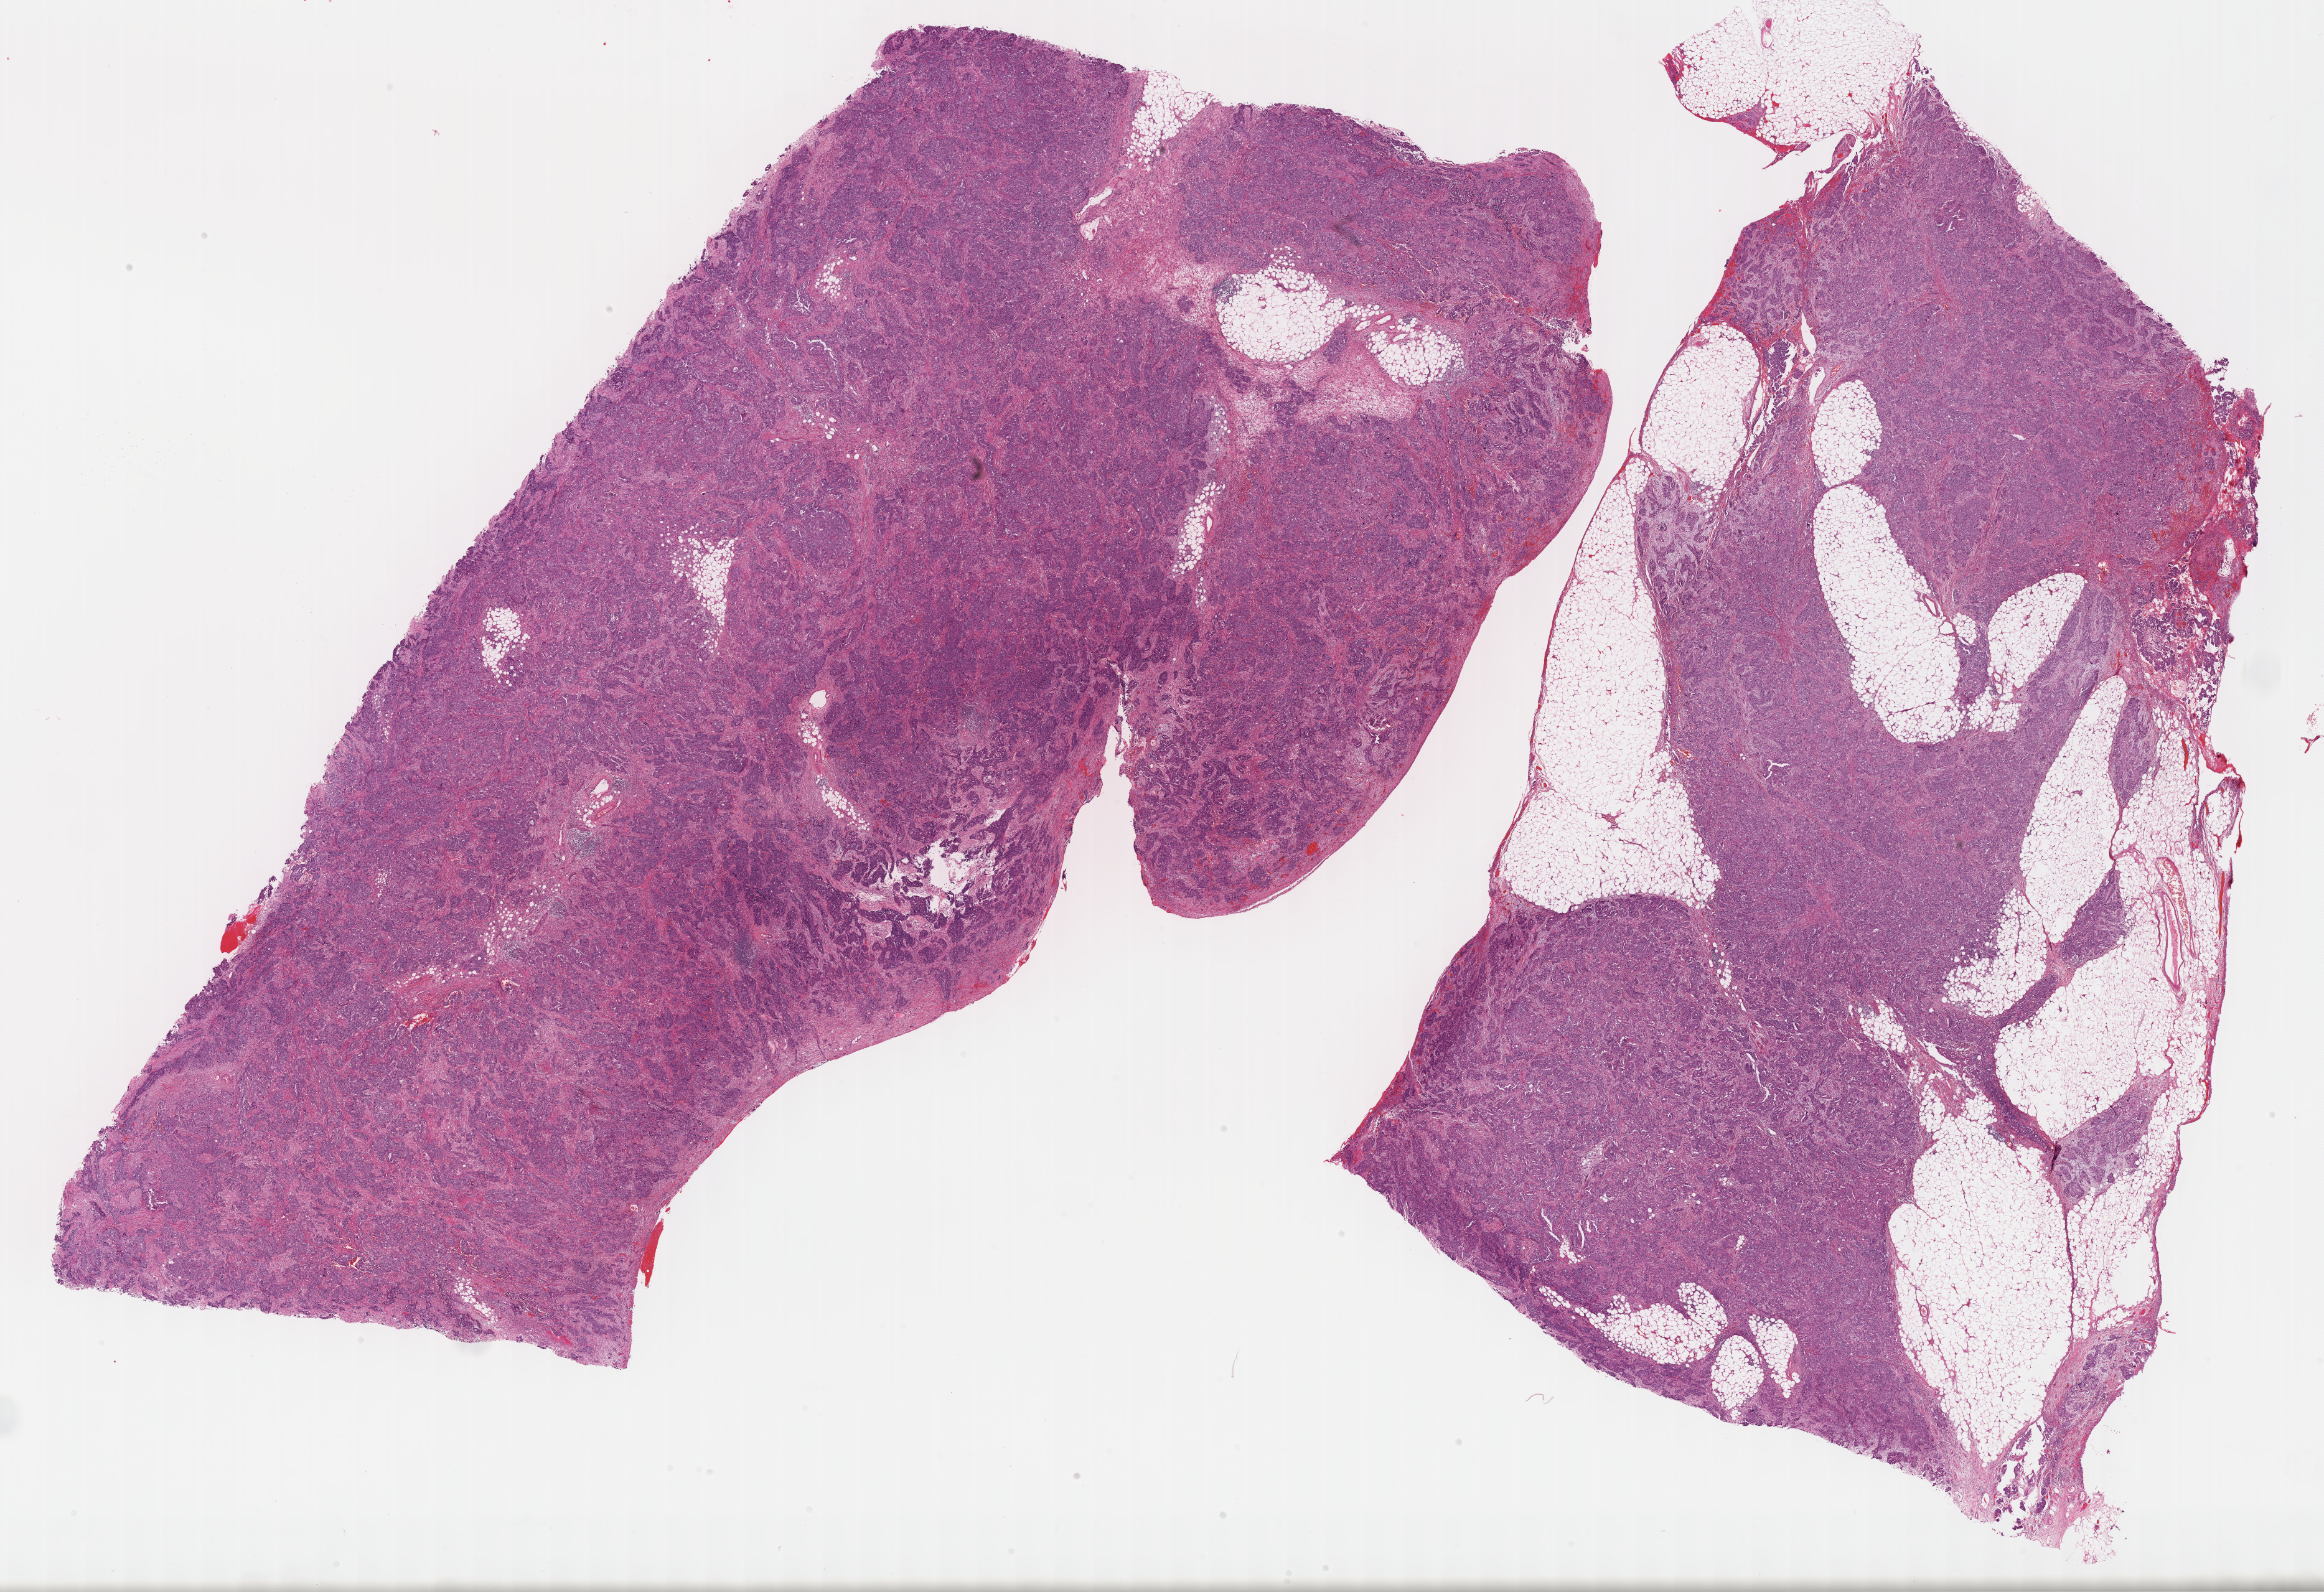
H&E whole-slide image, a low-resolution overview of the entire scanned area, about 30.2 x 20.7 mm, formalin-fixed paraffin-embedded (FFPE) diagnostic section, sample: primary tumour, ovary. Patient: female, age at initial diagnosis 49 years. Histologic grade: G3 (poorly differentiated).
Pathologic diagnosis: Serous cystadenocarcinoma, NOS. FIGO stage: IIIC.